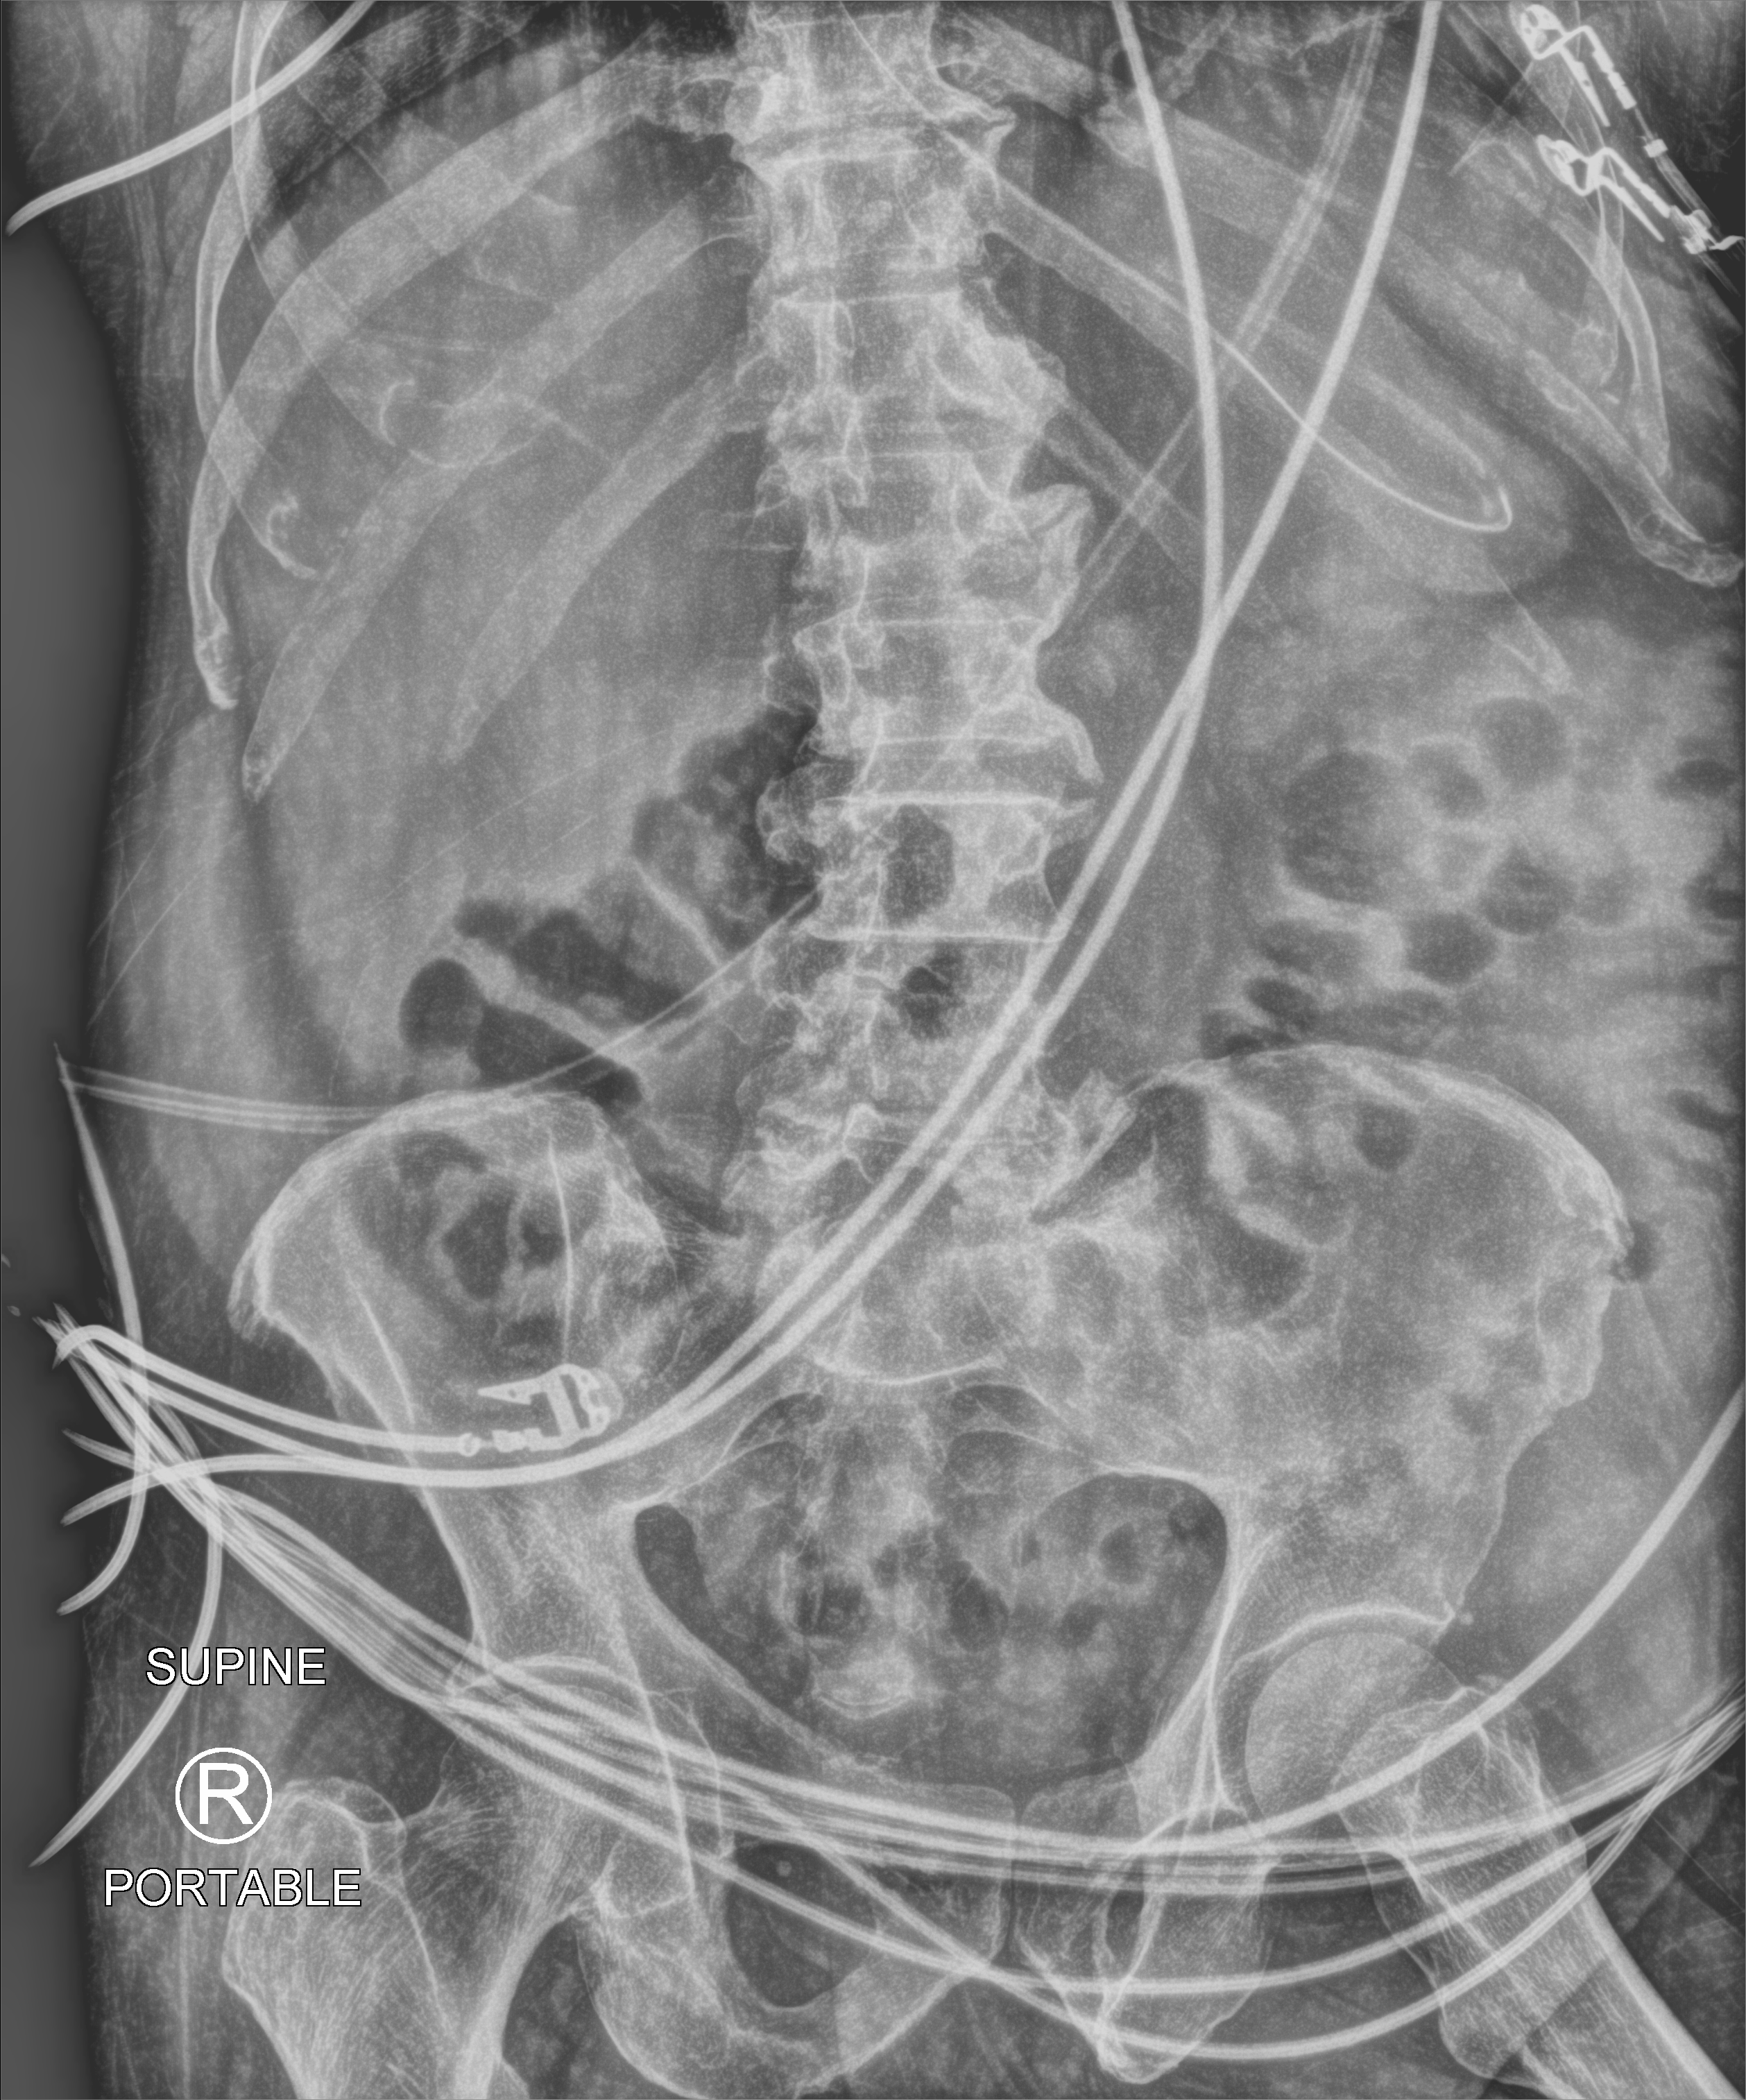
Abdomen X-ray (portable); anteroposterior (AP) projection. Male patient hospitalised with COVID-19, age 60–74 years.
Hospital-stay facts (about this admission, not read from this image; timing relative to this image not recorded):
- admitted to intensive care during this hospital stay: yes
- mechanically ventilated during this hospital stay: yes
- length of hospital stay: 31 days